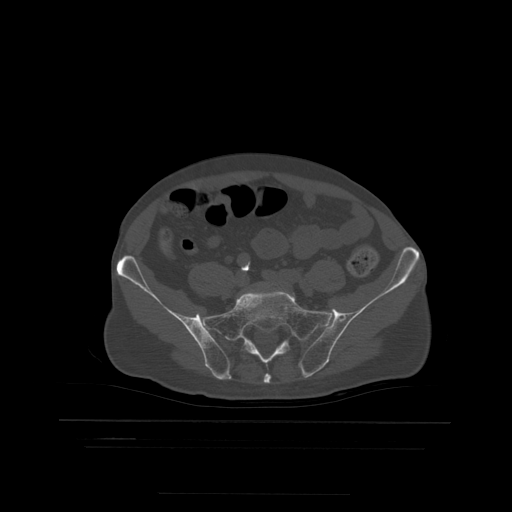
CT including the spine, one axial slice. Bone window (W 1800 / L 400 HU). 1.25 mm slice thickness. 512 × 512 image matrix, field of view 436 × 436 mm. Patient age 68 years. From the clinical record (not read from this slice): primary cancer: urothelial.
Annotated regions visible in this slice (semi-automatically segmented with operator editing):
- L5 vertebra: bounding box [x1, y1, x2, y2] px = [293, 293, 295, 296]